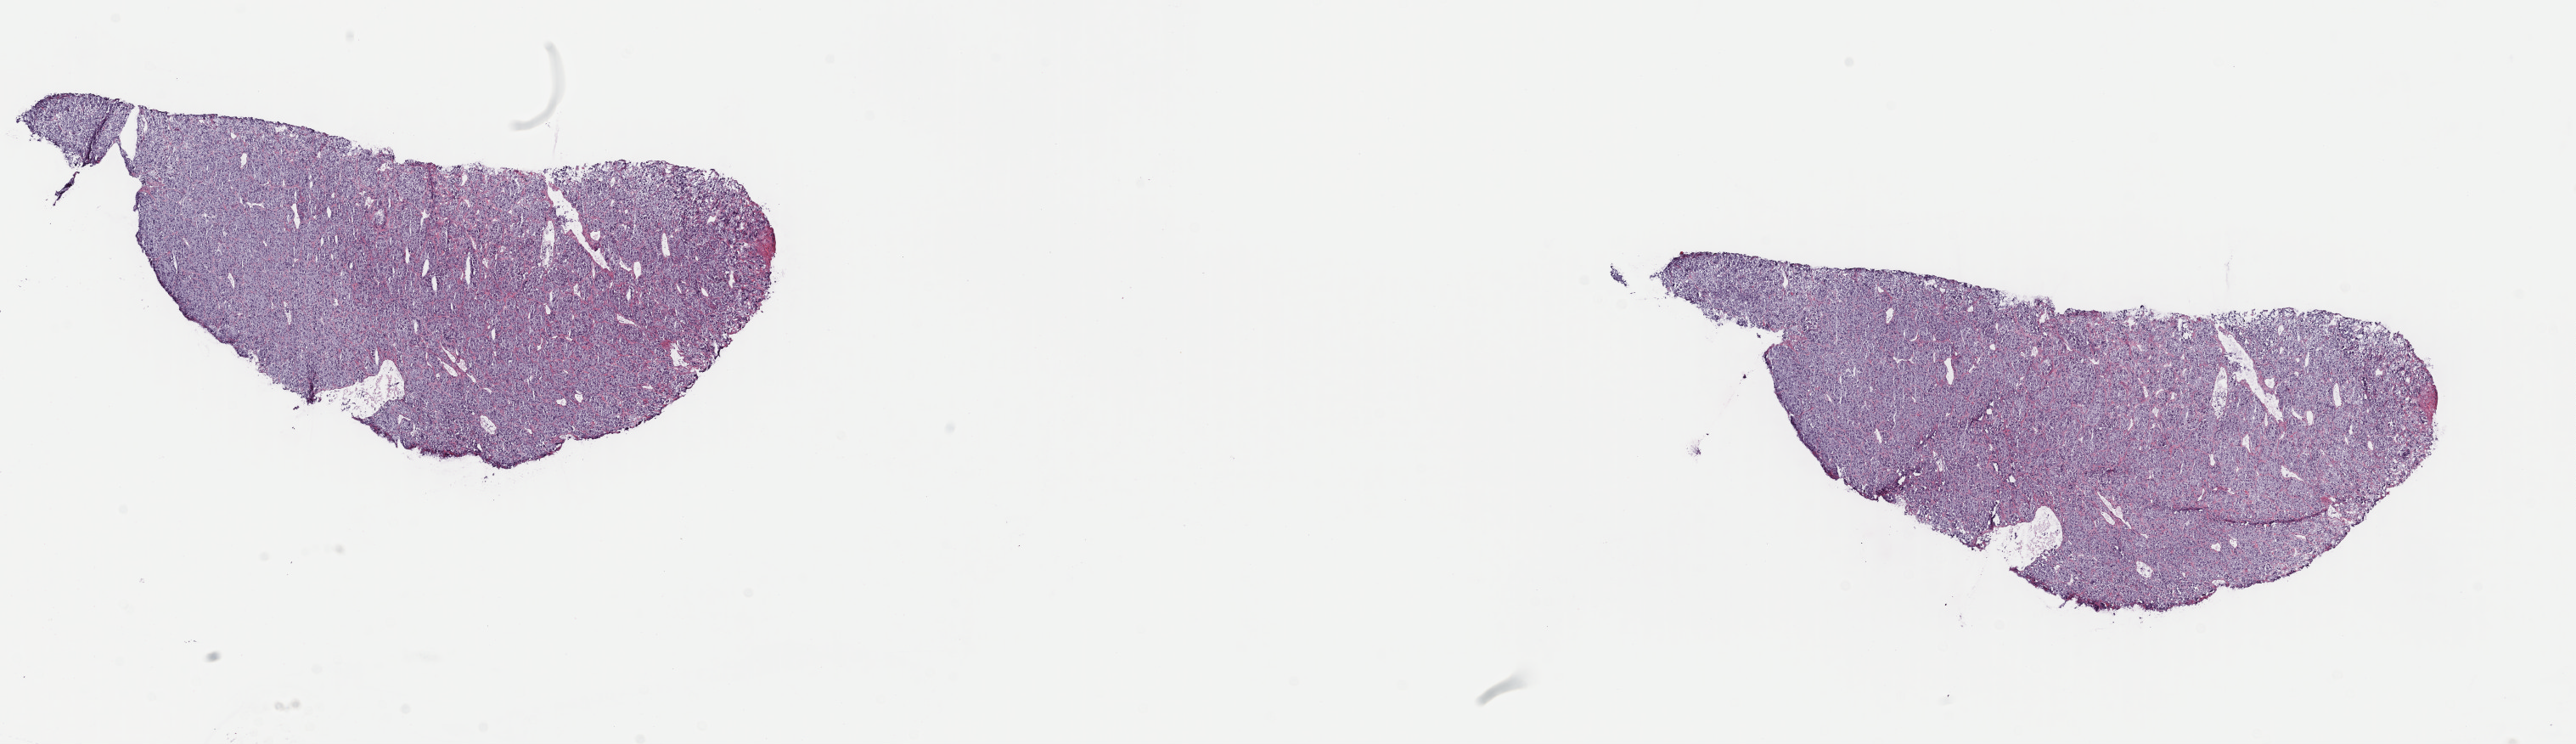
H&E whole-slide image, whole scanned area (about 23.9 x 6.9 mm, from a 40x scan) shown as a low-resolution overview; frozen section from the top of the tissue portion; primary tumour sample from the adrenal gland. Female, age 56 years at initial diagnosis. Slide review estimates, as recorded: tumour cells 85%, tumour nuclei 100%, normal cells 0%, stromal cells 15%, necrosis 0%. Infiltration values recorded for this section: lymphocyte infiltration 0%, monocyte infiltration 1%, neutrophil infiltration 0%.
Diagnosis: Pheochromocytoma, malignant.